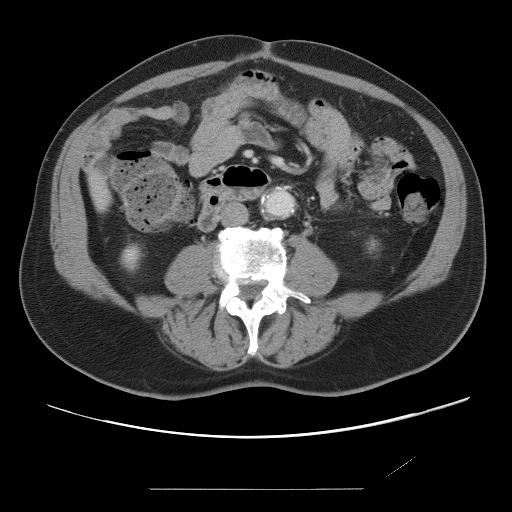
Contrast-enhanced abdominal CT, one axial slice; slice 7 of 87 in the series (ordered by position); 120 kVp; intravenous contrast given; soft-tissue window (W 400 / L 40 HU); 512 × 512 image matrix. Male patient, age 74 years. Case-level facts recorded for this patient, not image findings: diagnosis: colorectal cancer liver metastases, imaged before liver resection; multiple liver metastases: yes; largest metastasis: 1.1 cm; disease in both lobes: no.
Annotated regions visible in this slice (outlined manually by an expert reader):
- liver: bounding box <93,179,108,207> (left, top, right, bottom; pixels)
- planned liver remnant (the part of the liver to remain after resection): <93,179,108,207>